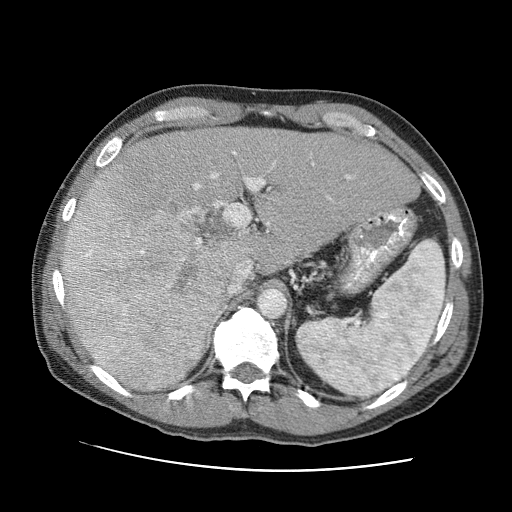
Contrast-enhanced abdominal CT (liver protocol), one axial slice. Reconstruction kernel STANDARD. One of 2 acquisitions stored at this slice position. Soft-tissue window (W 400 / L 40 HU). 2.5 mm slice thickness. 512 × 512 image matrix. Case-level facts recorded for this patient, not image findings: diagnosis: hepatocellular carcinoma (patient treated with transarterial chemoembolisation; whether this scan precedes or follows treatment is not stated here); TNM stage (as recorded): Stage-IVA; Child-Pugh class: A.
Outlined on this slice (semi-automatic segmentation, software-assisted and operator-edited):
- liver parenchyma outside the tumour (the mass and vessels are separate outlines, so this box may not span the whole liver): bounding box [x1, y1, x2, y2] px = [66, 126, 420, 390]
- mass: [61, 167, 241, 389]
- liver vessels: [143, 151, 351, 294]